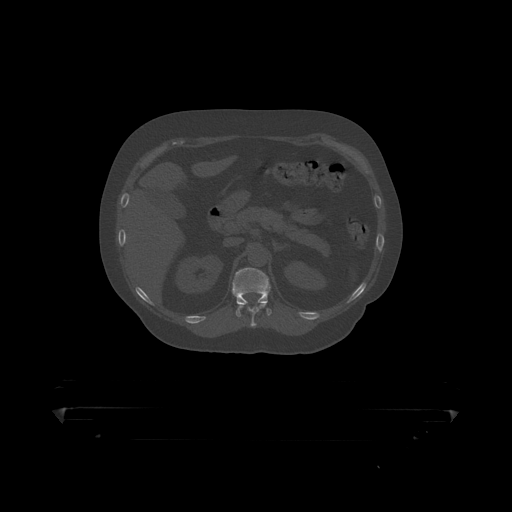
CT including the spine, one axial slice; reconstruction kernel STANDARD; 120 kVp; bone window (W 1800 / L 400 HU); 512 × 512 image matrix, field of view 650 × 650 mm. Male patient, age 60 years. From the clinical record (not read from this slice): primary cancer: prostate.
Outlined on this slice (semi-automatically segmented with operator editing):
- T11 vertebra: bounding box (x1, y1, x2, y2) in pixels: (241, 304, 267, 319)
- T12 vertebra: (232, 268, 272, 317)